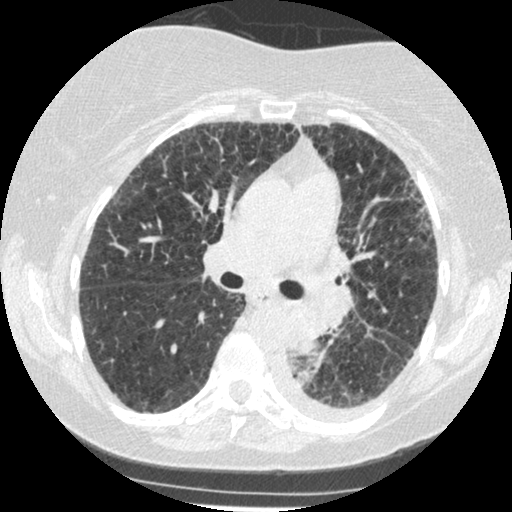
Low-dose screening chest CT, one axial slice. Position 157 of 341 along the scan axis. Lung window (W 1500 / L -600 HU). 1.25 mm slice thickness. 512 × 512 image matrix, field of view 310 × 310 mm.
Outlined on this slice (manually delineated by an expert):
- lesion 1 (tumor, lower lobe of left lung): bounding box (x1, y1, x2, y2) in pixels: (290, 306, 327, 355)